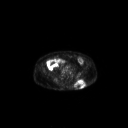
FDG PET of an extremity soft-tissue mass (from a PET/CT study), one axial slice. Slice 85 of 267 in the series (ordered by position). 3.27 mm slice thickness. 128 × 128 image matrix, field of view 700 × 700 mm. Patient: male, 69 years. Case-level facts recorded for this patient, not image findings: histological type: leiomyosarcoma; grade: intermediate; site of the primary tumour: left pelvis.
Annotated regions visible in this slice (expert contour drawn on MRI and transferred to this co-registered scan by the dataset authors):
- gross tumour volume (mass): box from (x=74, y=78) to (x=86, y=89) px